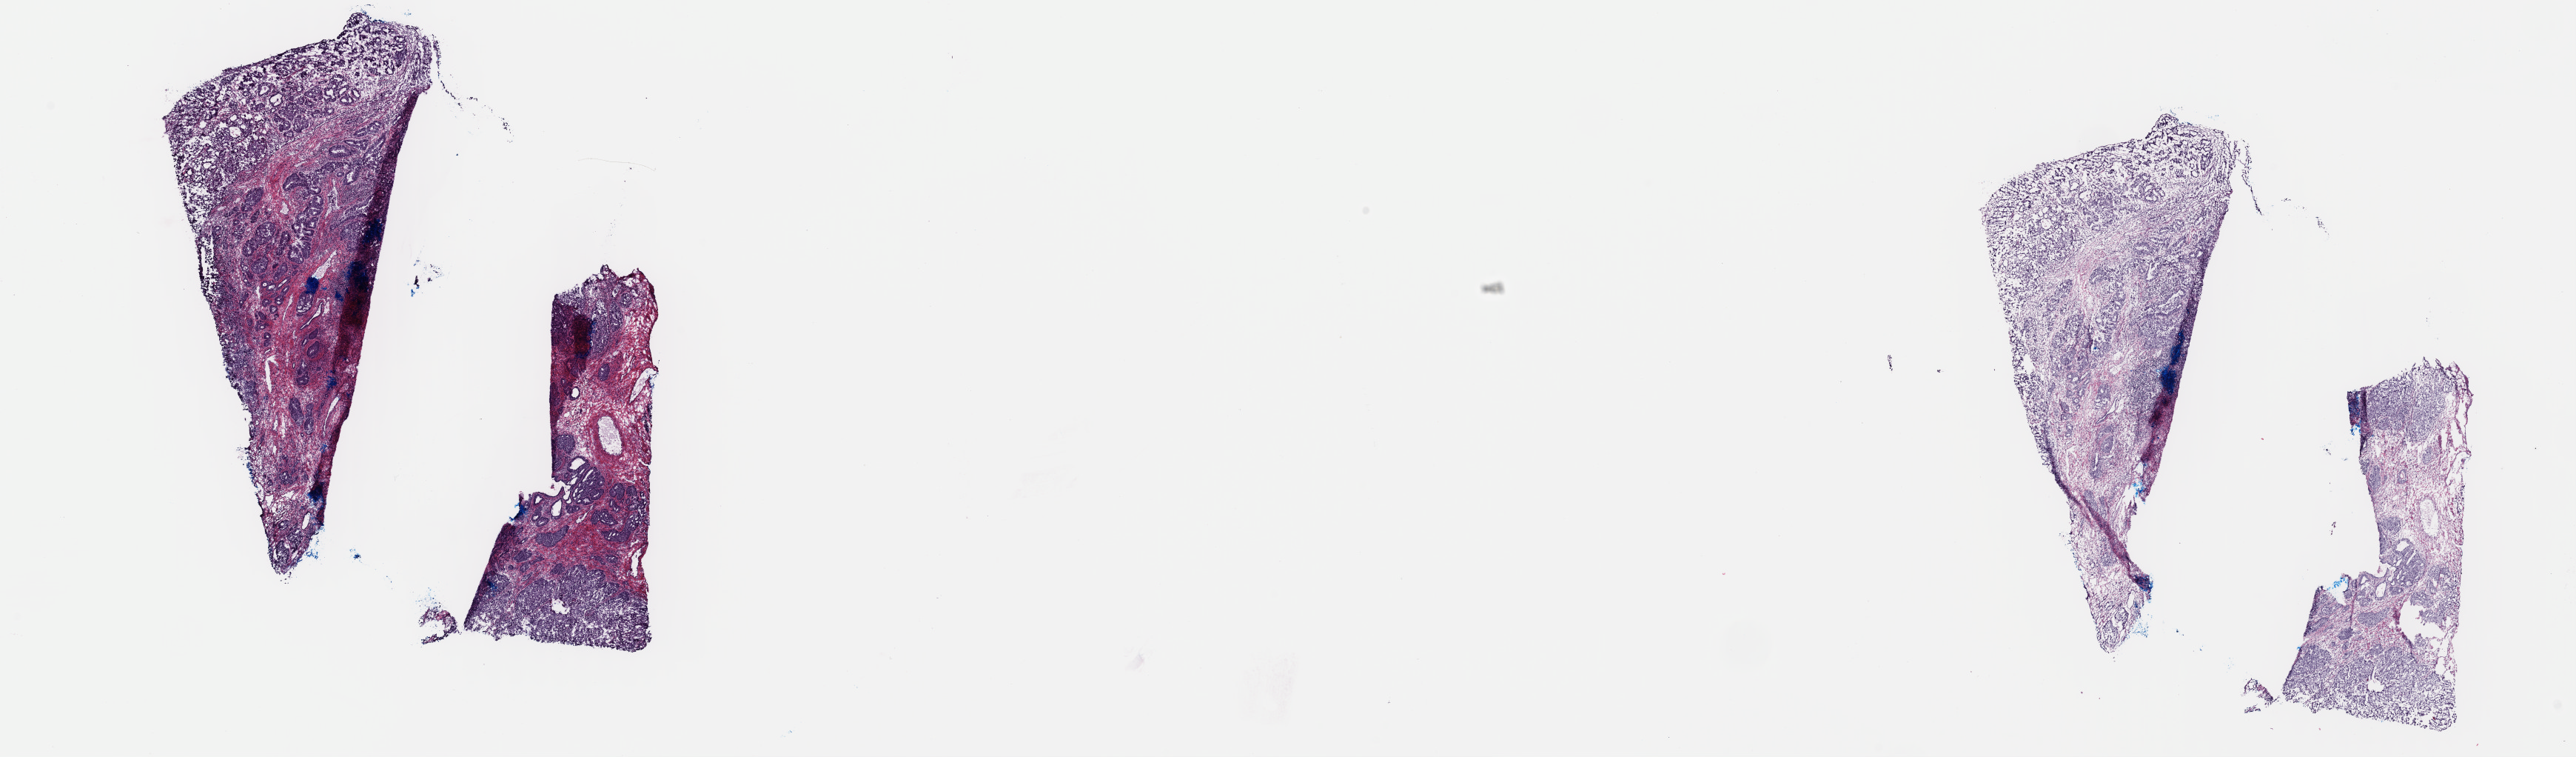
H&E whole-slide image — a low-resolution overview of the entire scanned area, about 27.5 x 8.1 mm (from a 40x scan). Frozen section from the top of the tissue portion. Sample: primary tumour, uterus. Female, age 65 years at initial diagnosis. Slide review estimates, as recorded: tumour cells 60%, tumour nuclei 60%.
Diagnosis: Endometrioid adenocarcinoma, NOS (endometrium).